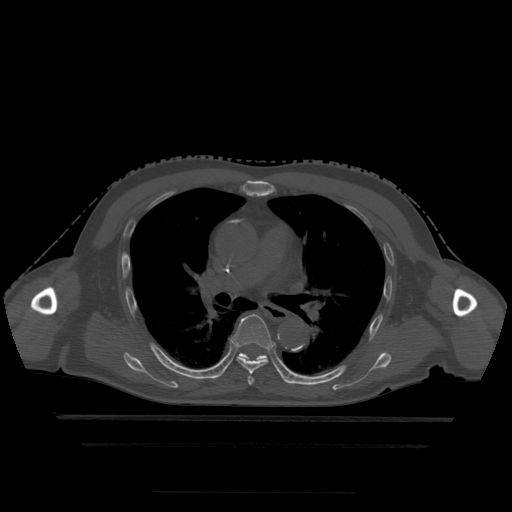
CT including the spine, one axial slice. Slice 314 of 522 in the series (ordered by position). Bone window (W 1800 / L 400 HU). 1.25 mm slice thickness. 512 × 512 image matrix, field of view 436 × 436 mm. Patient age 68 years. Case-level facts recorded for this patient, not image findings: primary cancer: urothelial.
Outlined on this slice (semi-automatic segmentation, software-assisted and operator-edited):
- T5 vertebra: bounding box [x1, y1, x2, y2] px = [248, 377, 254, 385]
- T6 vertebra: [232, 315, 273, 375]
- T7 vertebra: [239, 353, 281, 375]